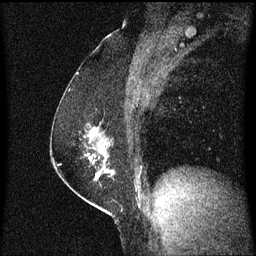
Breast MRI (dynamic contrast-enhanced), one sagittal slice; slice 37 of 60 in the series (ordered by position); dynamic contrast-enhanced series, image 2 of 3 at this slice position (ordered by acquisition); 1.5 T; TE 4.2 ms, TR 8.4 ms; 2 mm slice thickness; 256 × 256 image matrix, field of view 200 × 200 mm. Patient: female, 52 years. From the clinical record (not read from this slice): setting: breast cancer imaged before/during neoadjuvant chemotherapy; receptor status: HER2-positive.
Outlined on this slice (semi-automatically segmented with operator editing):
- analysis volume of interest (the breast-tissue region the enhancement analysis was run in; not a lesion): bounding box [x1, y1, x2, y2] px = [67, 120, 108, 187]
- tumour enhancement mask (voxels above the 70 % enhancement threshold inside the analysis volume of interest): [91, 128, 98, 137]